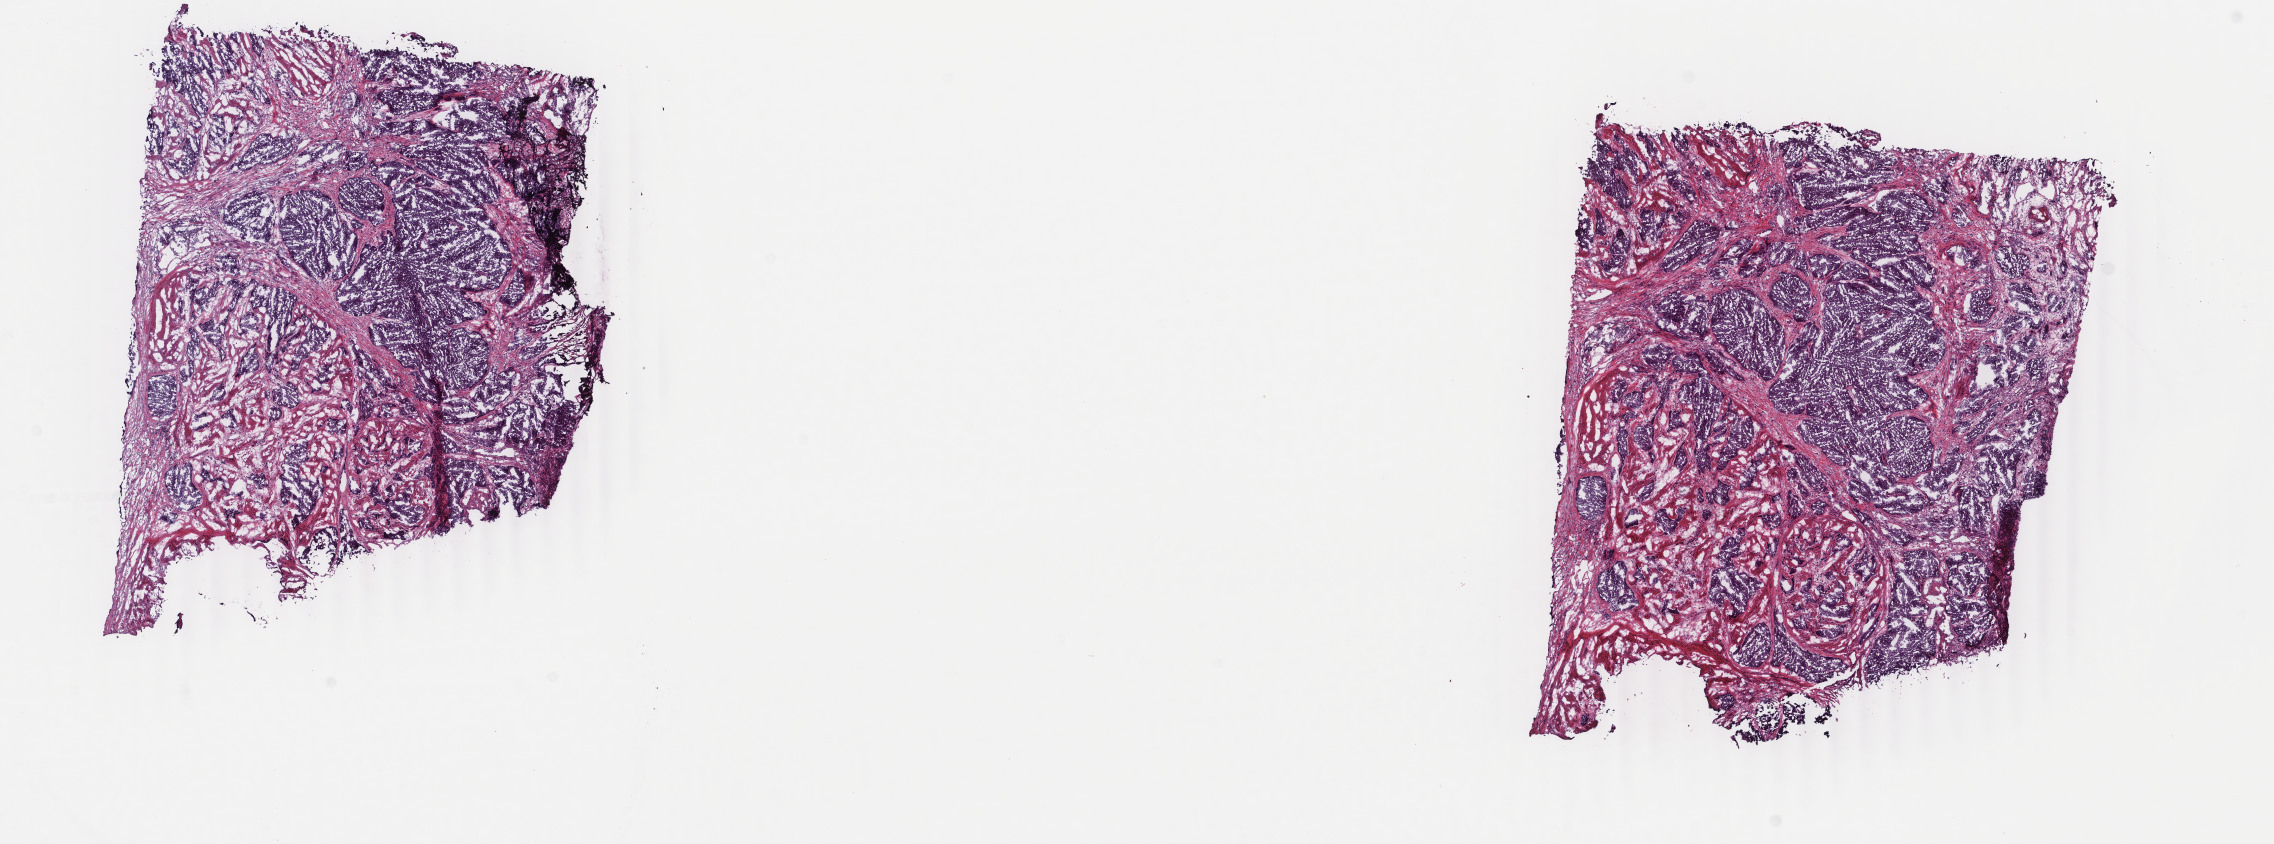
Hematoxylin and eosin (H&E) stained whole-slide image — shown as a low-resolution overview of the whole scanned area (about 18.1 x 6.7 mm). Frozen section from the top of the tissue portion. Primary tumour sample from the bladder. Patient: male, age at initial diagnosis 84 years. Histologic grade: high grade. Slide review estimates, as recorded: tumour cells 80%, tumour nuclei 80%, normal cells 0%, stromal cells 20%, necrosis 0%. Infiltration values recorded for this section: lymphocyte infiltration 2%, monocyte infiltration 1%, neutrophil infiltration 1%.
- pathologic diagnosis: Transitional cell carcinoma
- lymph nodes positive (case pathology): 0 of 11 examined
- AJCC pathologic stage: III (6th edition)